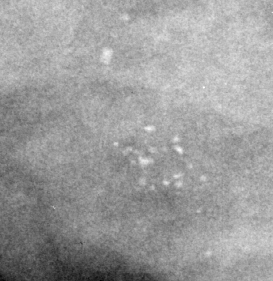
Region of interest cut from a scanned film mammogram (one marked finding), right breast, CC view.
- Marked abnormality: calcifications, morphology punctate / pleomorphic, distribution clustered; BI-RADS assessment category 4; subtlety rating 2 on a 1 (subtle) to 5 (obvious) scale; pathology result (as recorded, not read from the image): benign.